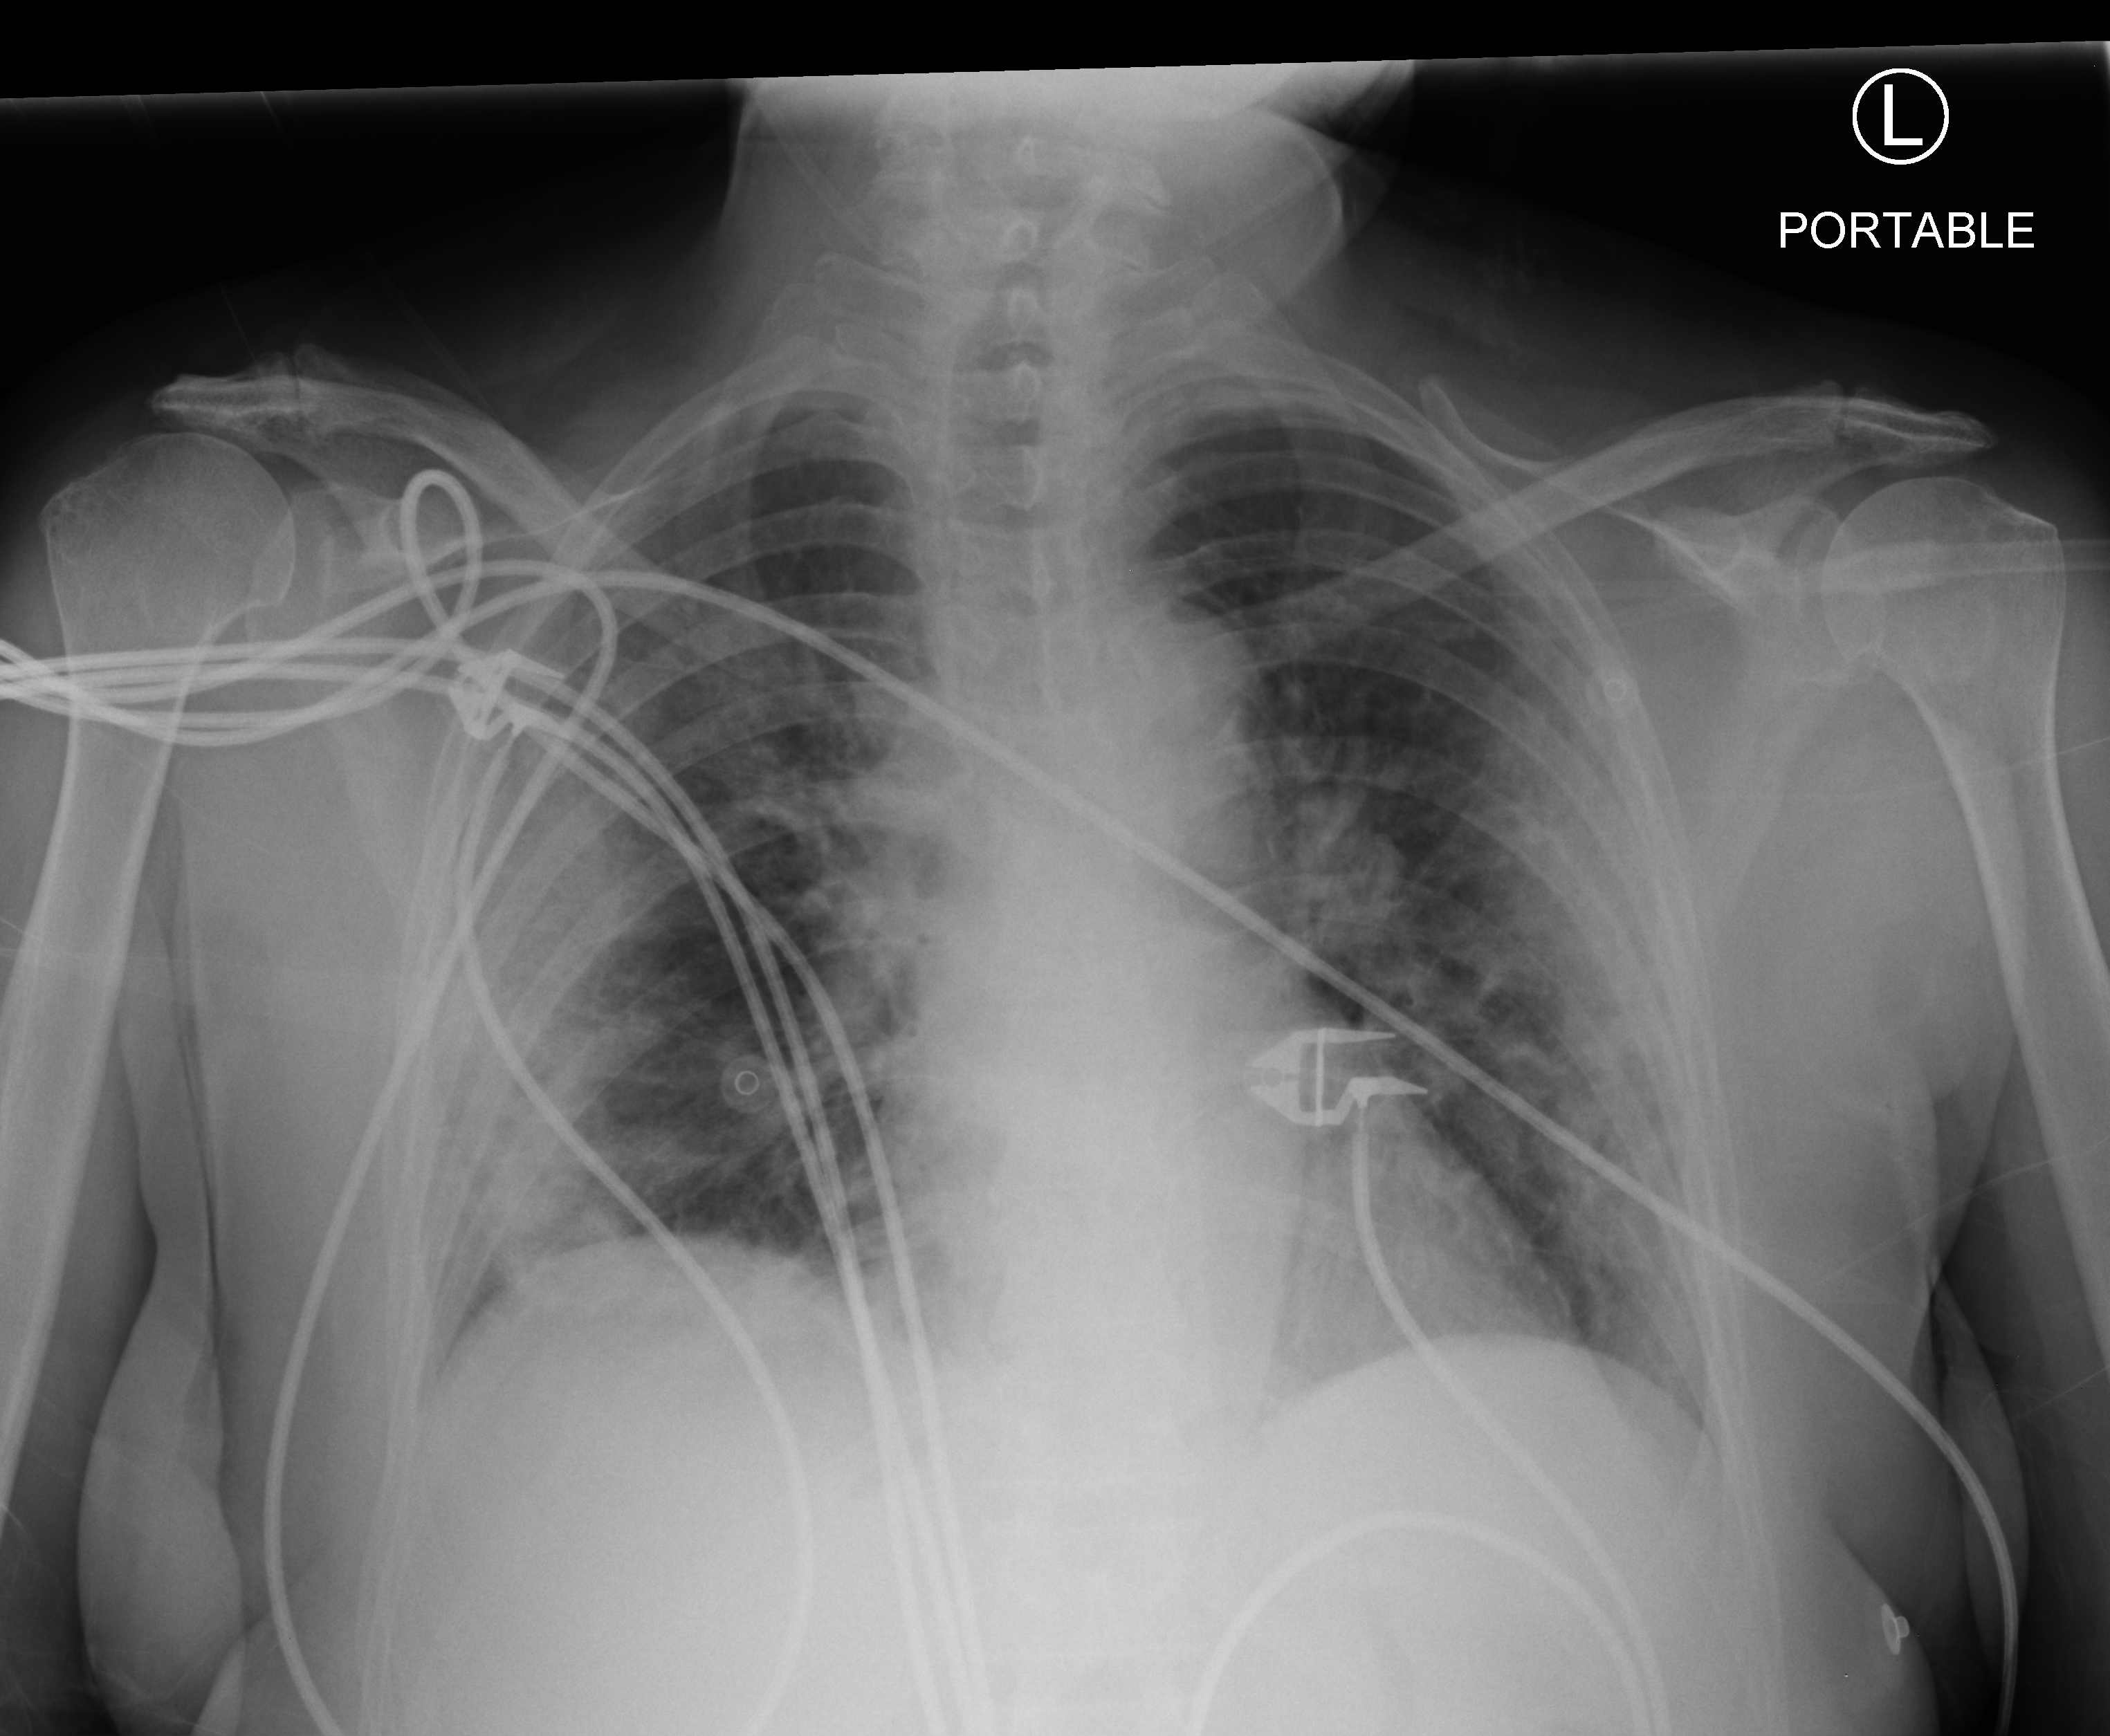
Chest X-ray (portable); anteroposterior (AP) projection. Female patient hospitalised with COVID-19, age 60–74 years.
From the hospital-stay record, not from the radiograph (when in the stay this image was taken is not recorded): admitted to intensive care during this hospital stay: yes.